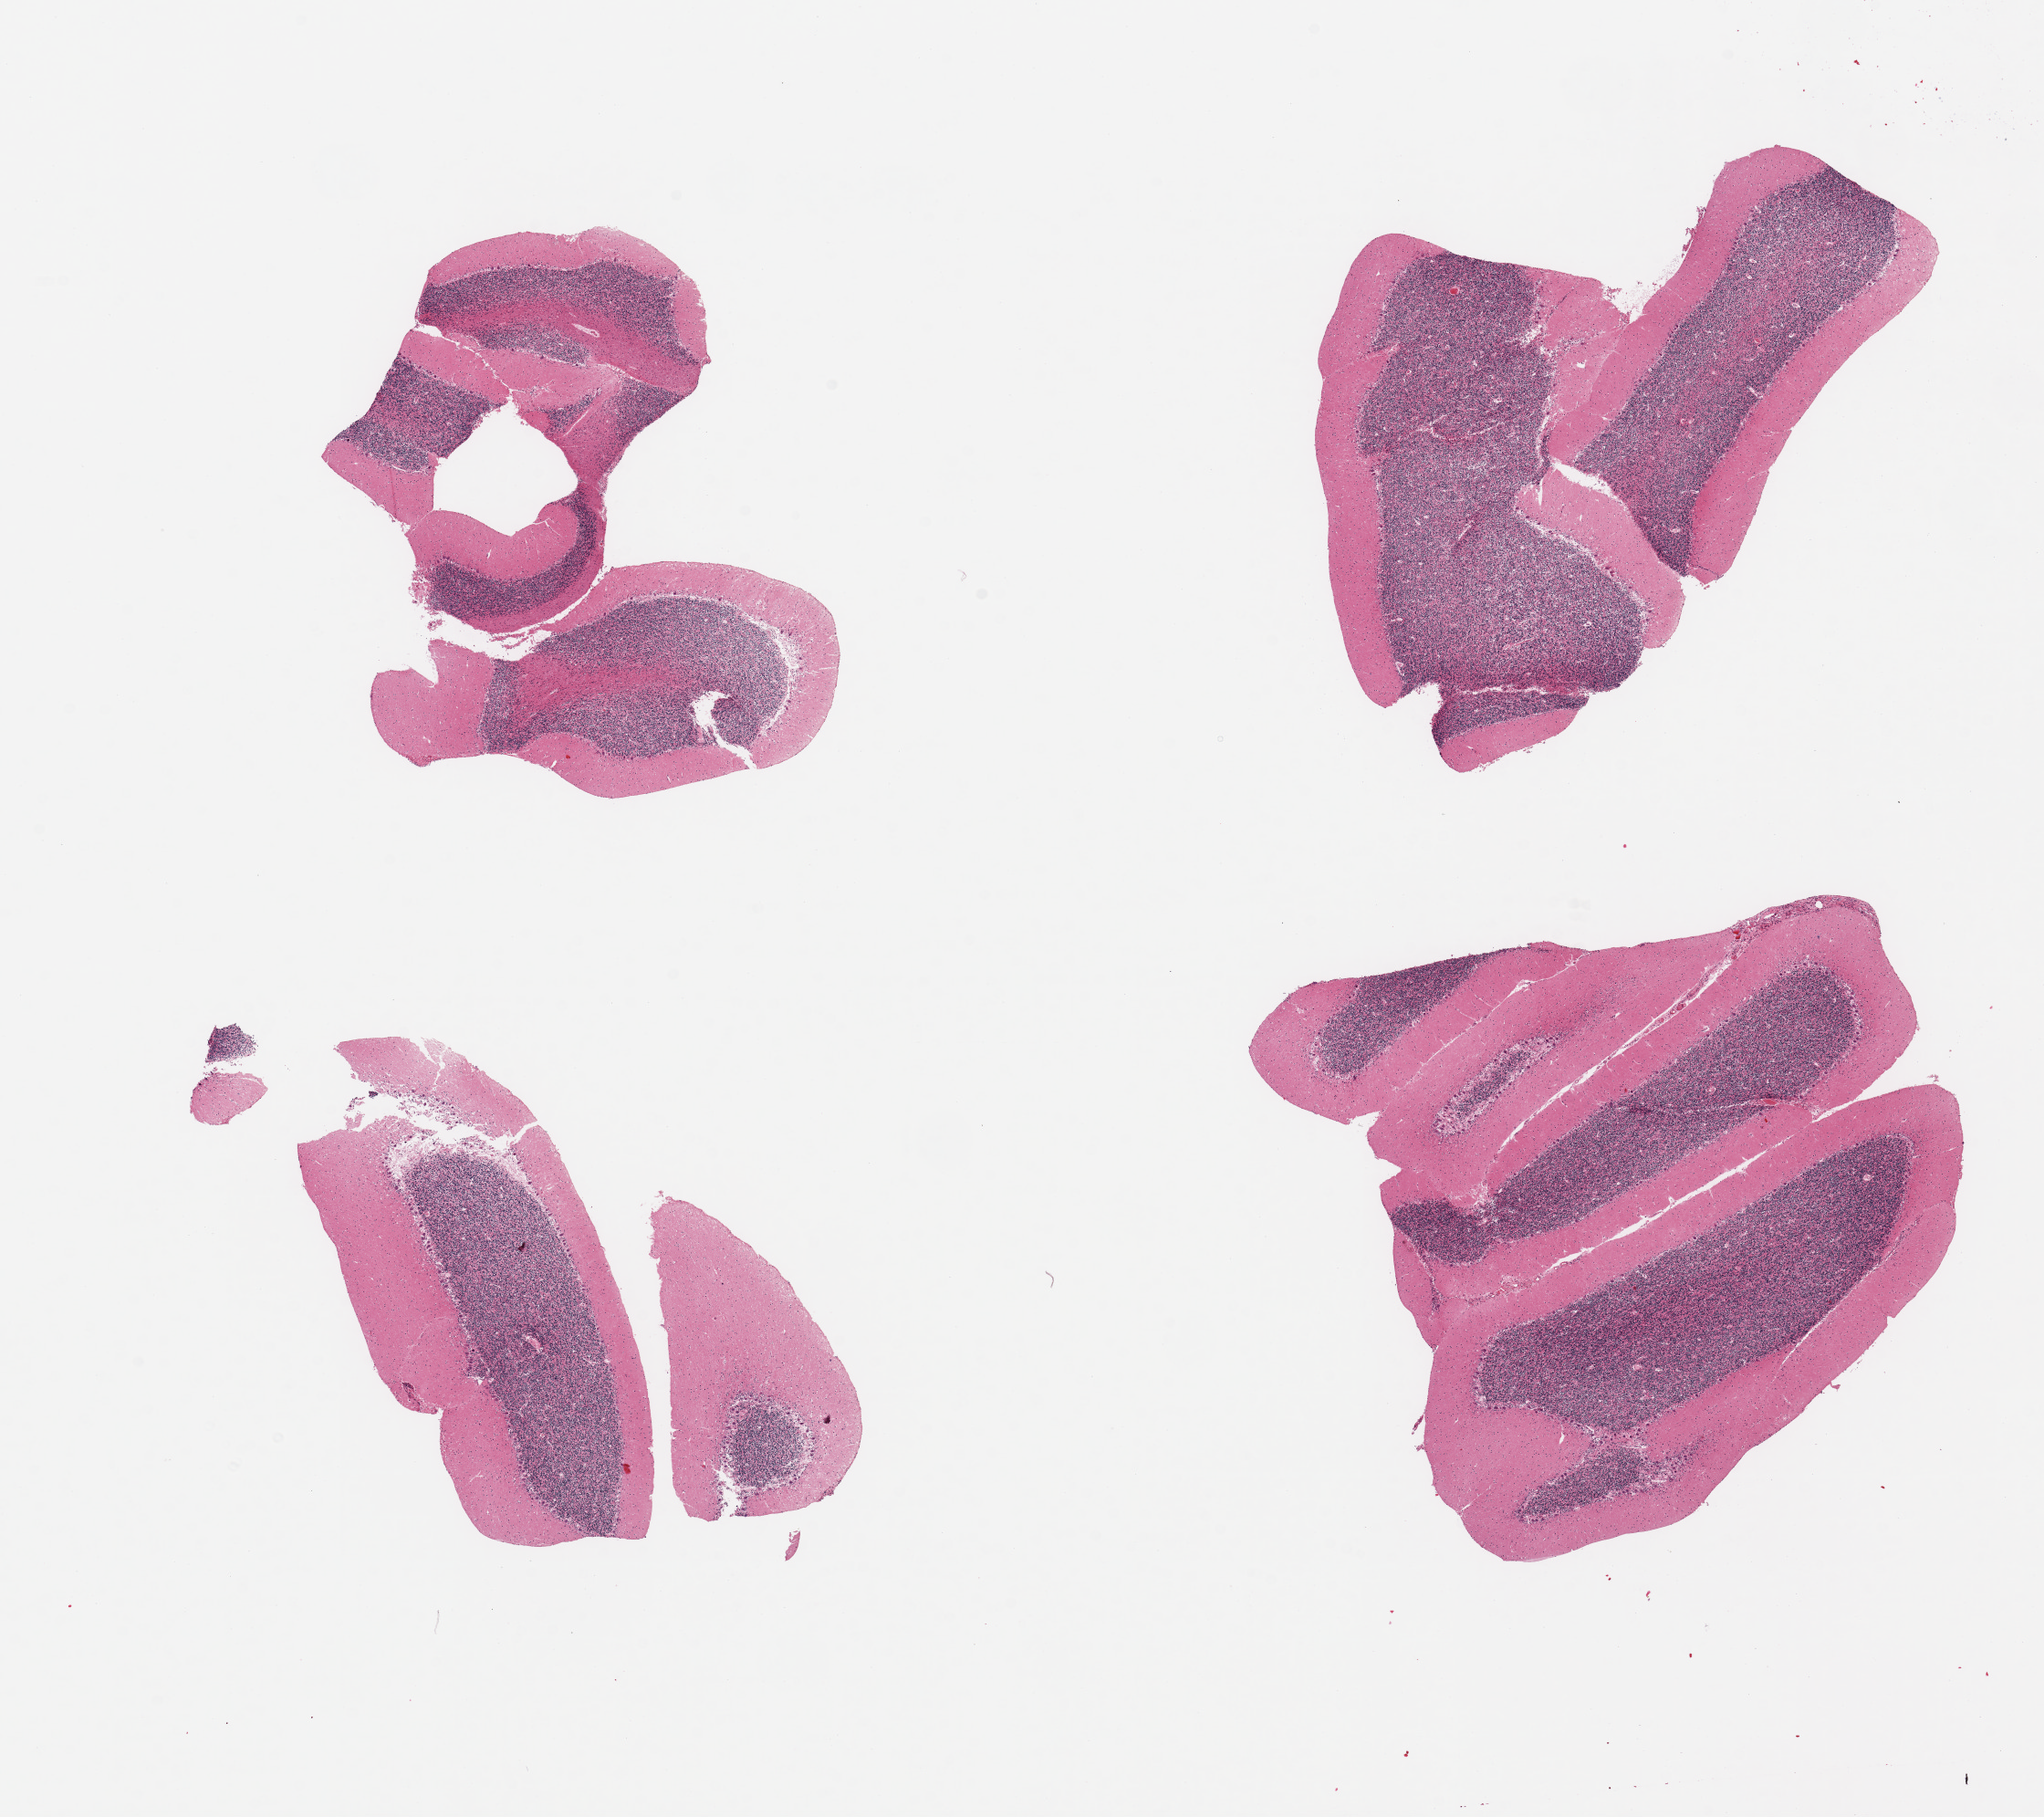
Digitized haematoxylin and eosin-stained section, low-resolution overview of the scanned area, about 17.7 x 15.7 mm (acquisition: 20x scan). PAXgene-fixed, paraffin-embedded tissue. Section of cerebellum (target tissue). Tissue donor sample. Female donor.
Reviewer comment on this tissue sample: 4 pieces, no abnormalities.